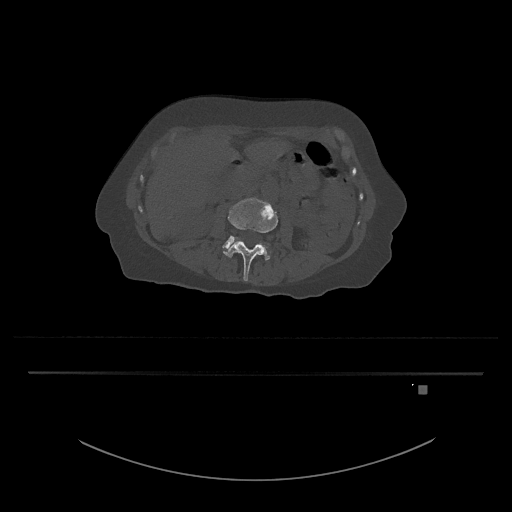
CT including the spine, one axial slice; position 413 of 797 along the scan axis; bone window (W 1800 / L 400 HU); 0.5 mm slice thickness; 512 × 512 image matrix, field of view 500 × 500 mm. Female patient, age 57 years. Case-level facts recorded for this patient, not image findings: primary cancer: cervical.
Outlined on this slice (semi-automatic segmentation, software-assisted and operator-edited):
- L3 vertebra: box from (x=223, y=198) to (x=279, y=281) px
- L4 vertebra: (x=222, y=235)–(x=271, y=260)